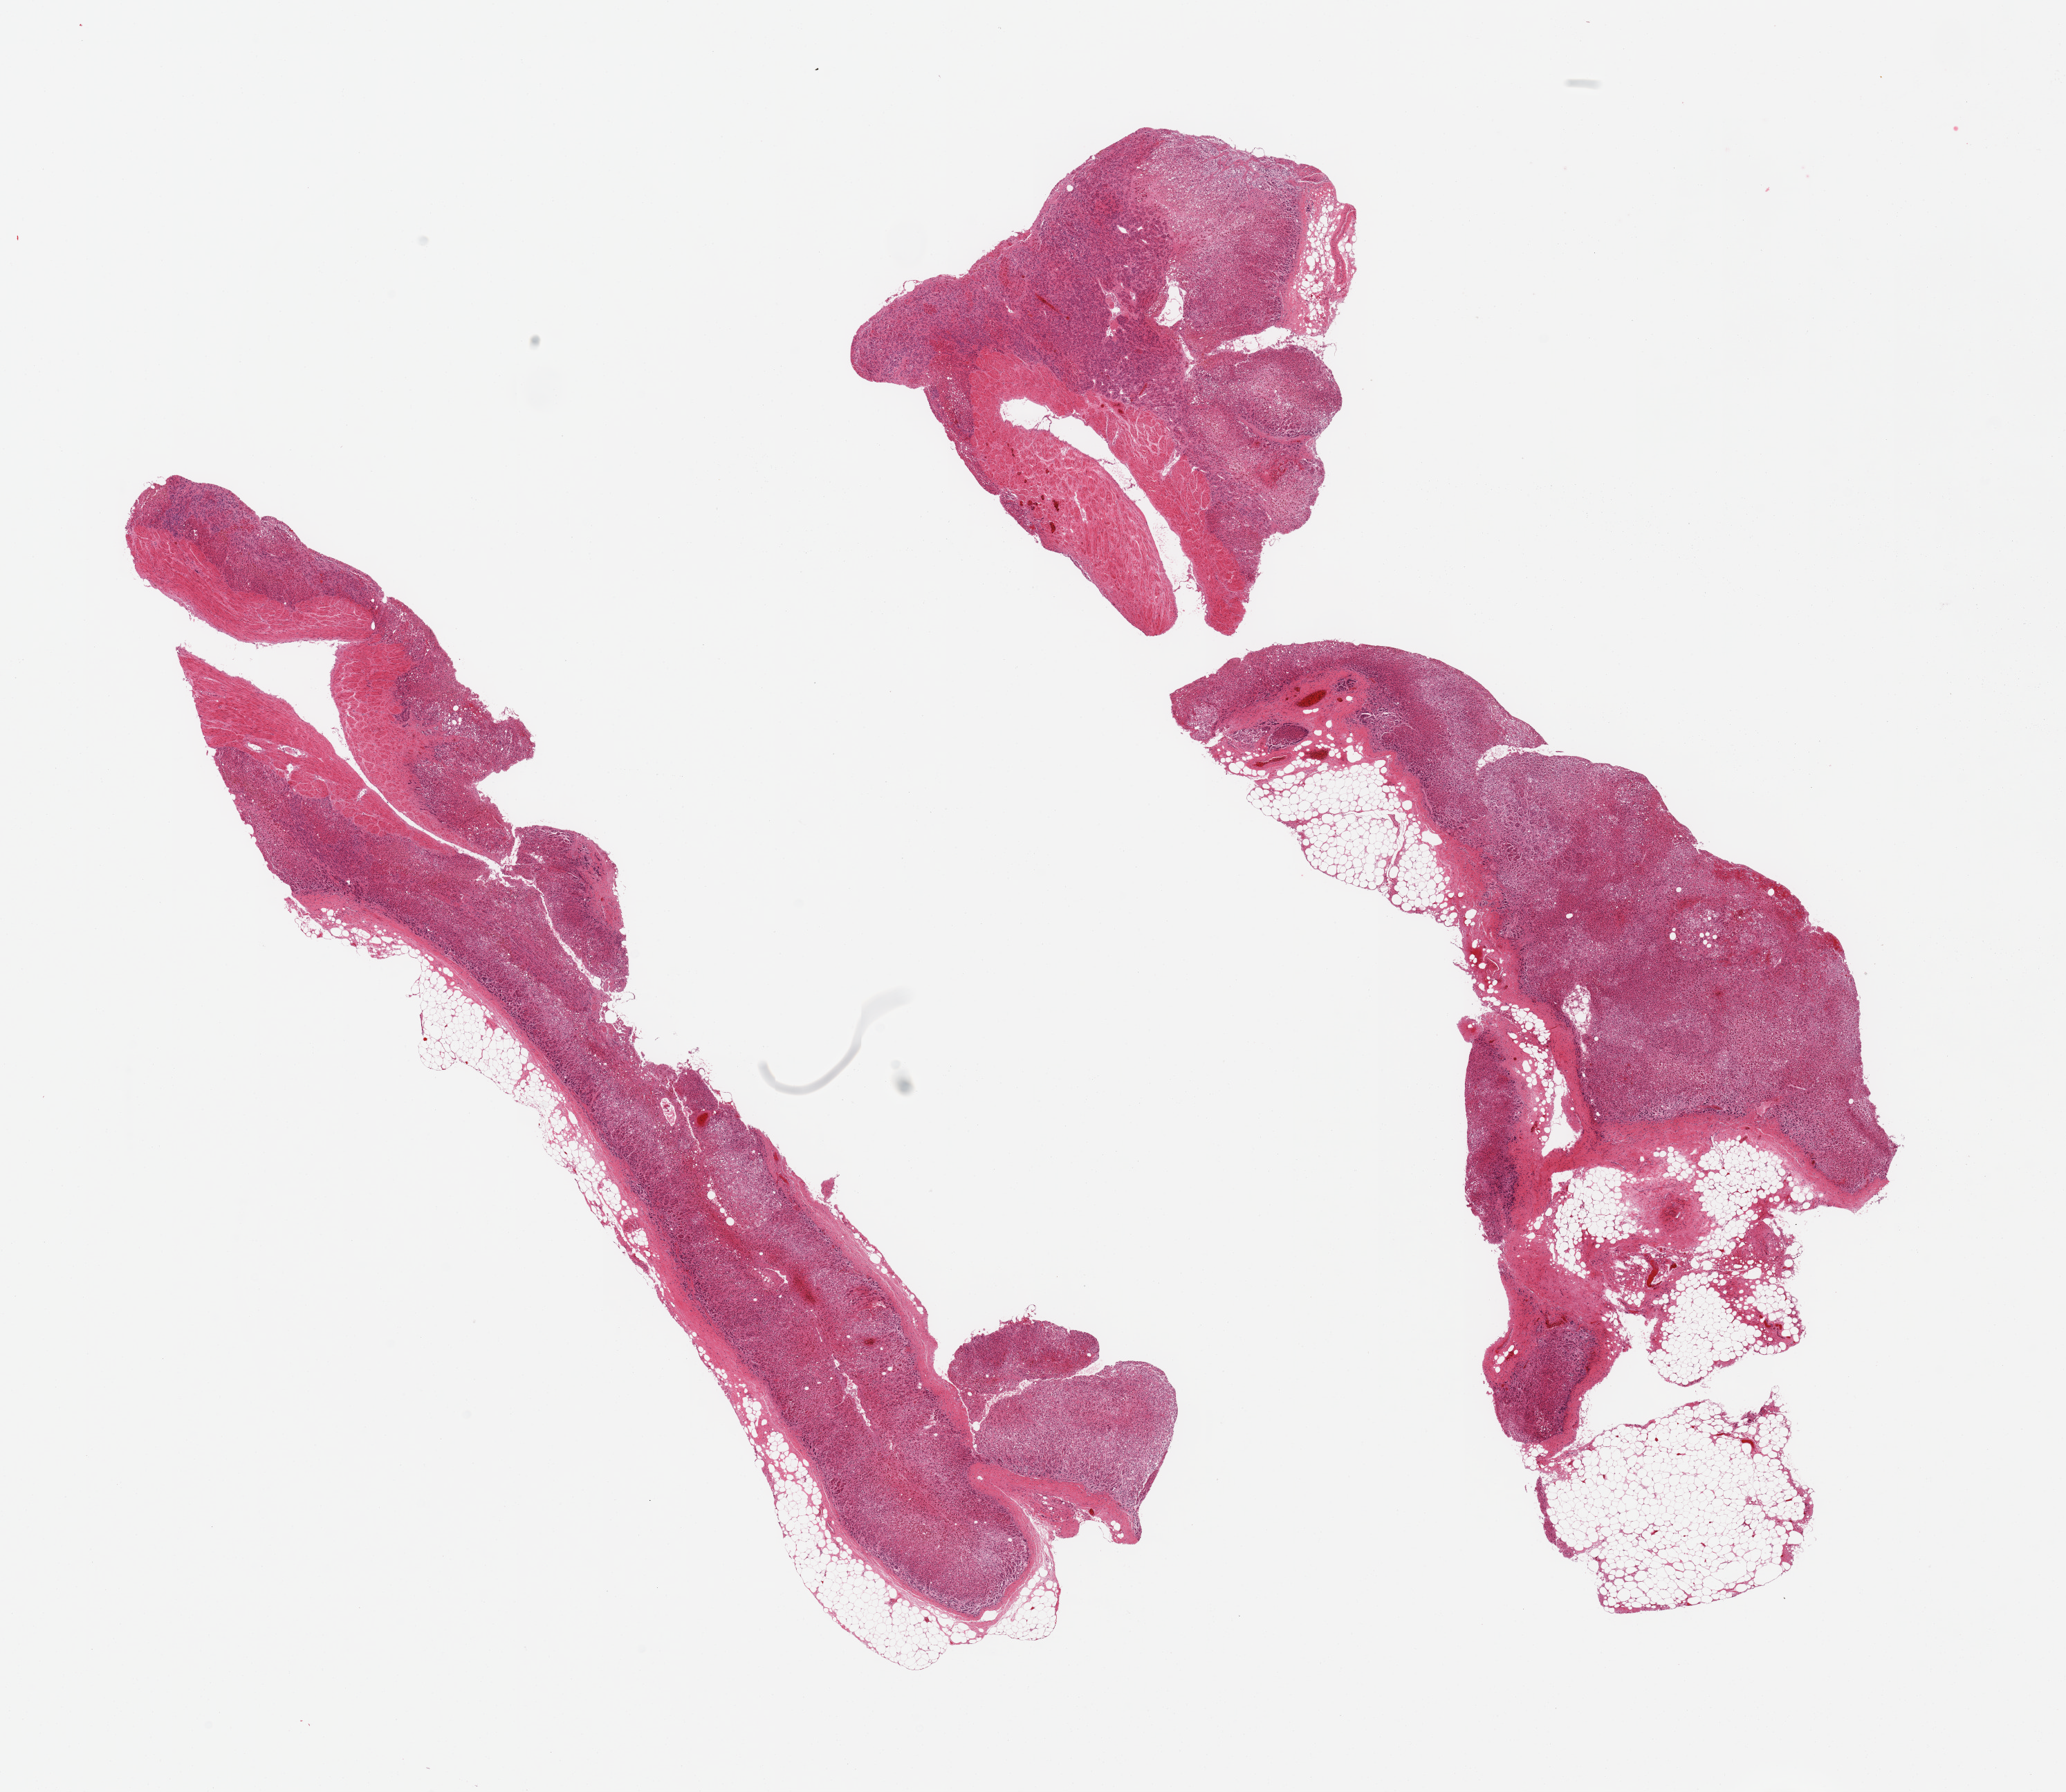
Whole-slide image, haematoxylin and eosin stain, shown as a low-resolution overview of the whole scanned area (about 23.6 x 20.5 mm), PAXgene-fixed, paraffin-embedded tissue, target tissue: adrenal gland, tissue donor sample. Donor sex: male.
Pathologist's review note for this sample: 2 pieces; 10 and 20% attached fat and vessels.